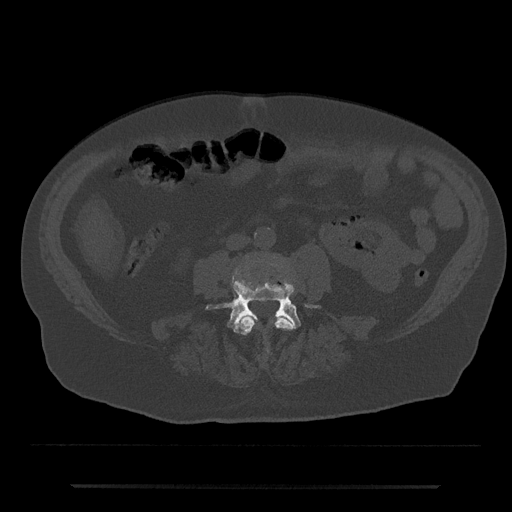
CT including the spine, one axial slice. Position 369 of 797 along the scan axis. Bone window (W 1800 / L 400 HU). 0.5 mm slice thickness. 512 × 512 image matrix, field of view 434 × 434 mm. Male patient, age 80 years. Case-level facts recorded for this patient, not image findings: primary cancer: prostate; vertebrae with lytic lesions (as recorded): L1, T11.
Structures marked on this image (semi-automatic segmentation, software-assisted and operator-edited):
- L3 vertebra: box from (x=236, y=315) to (x=294, y=335) px
- L4 vertebra: (x=205, y=280)–(x=320, y=332)